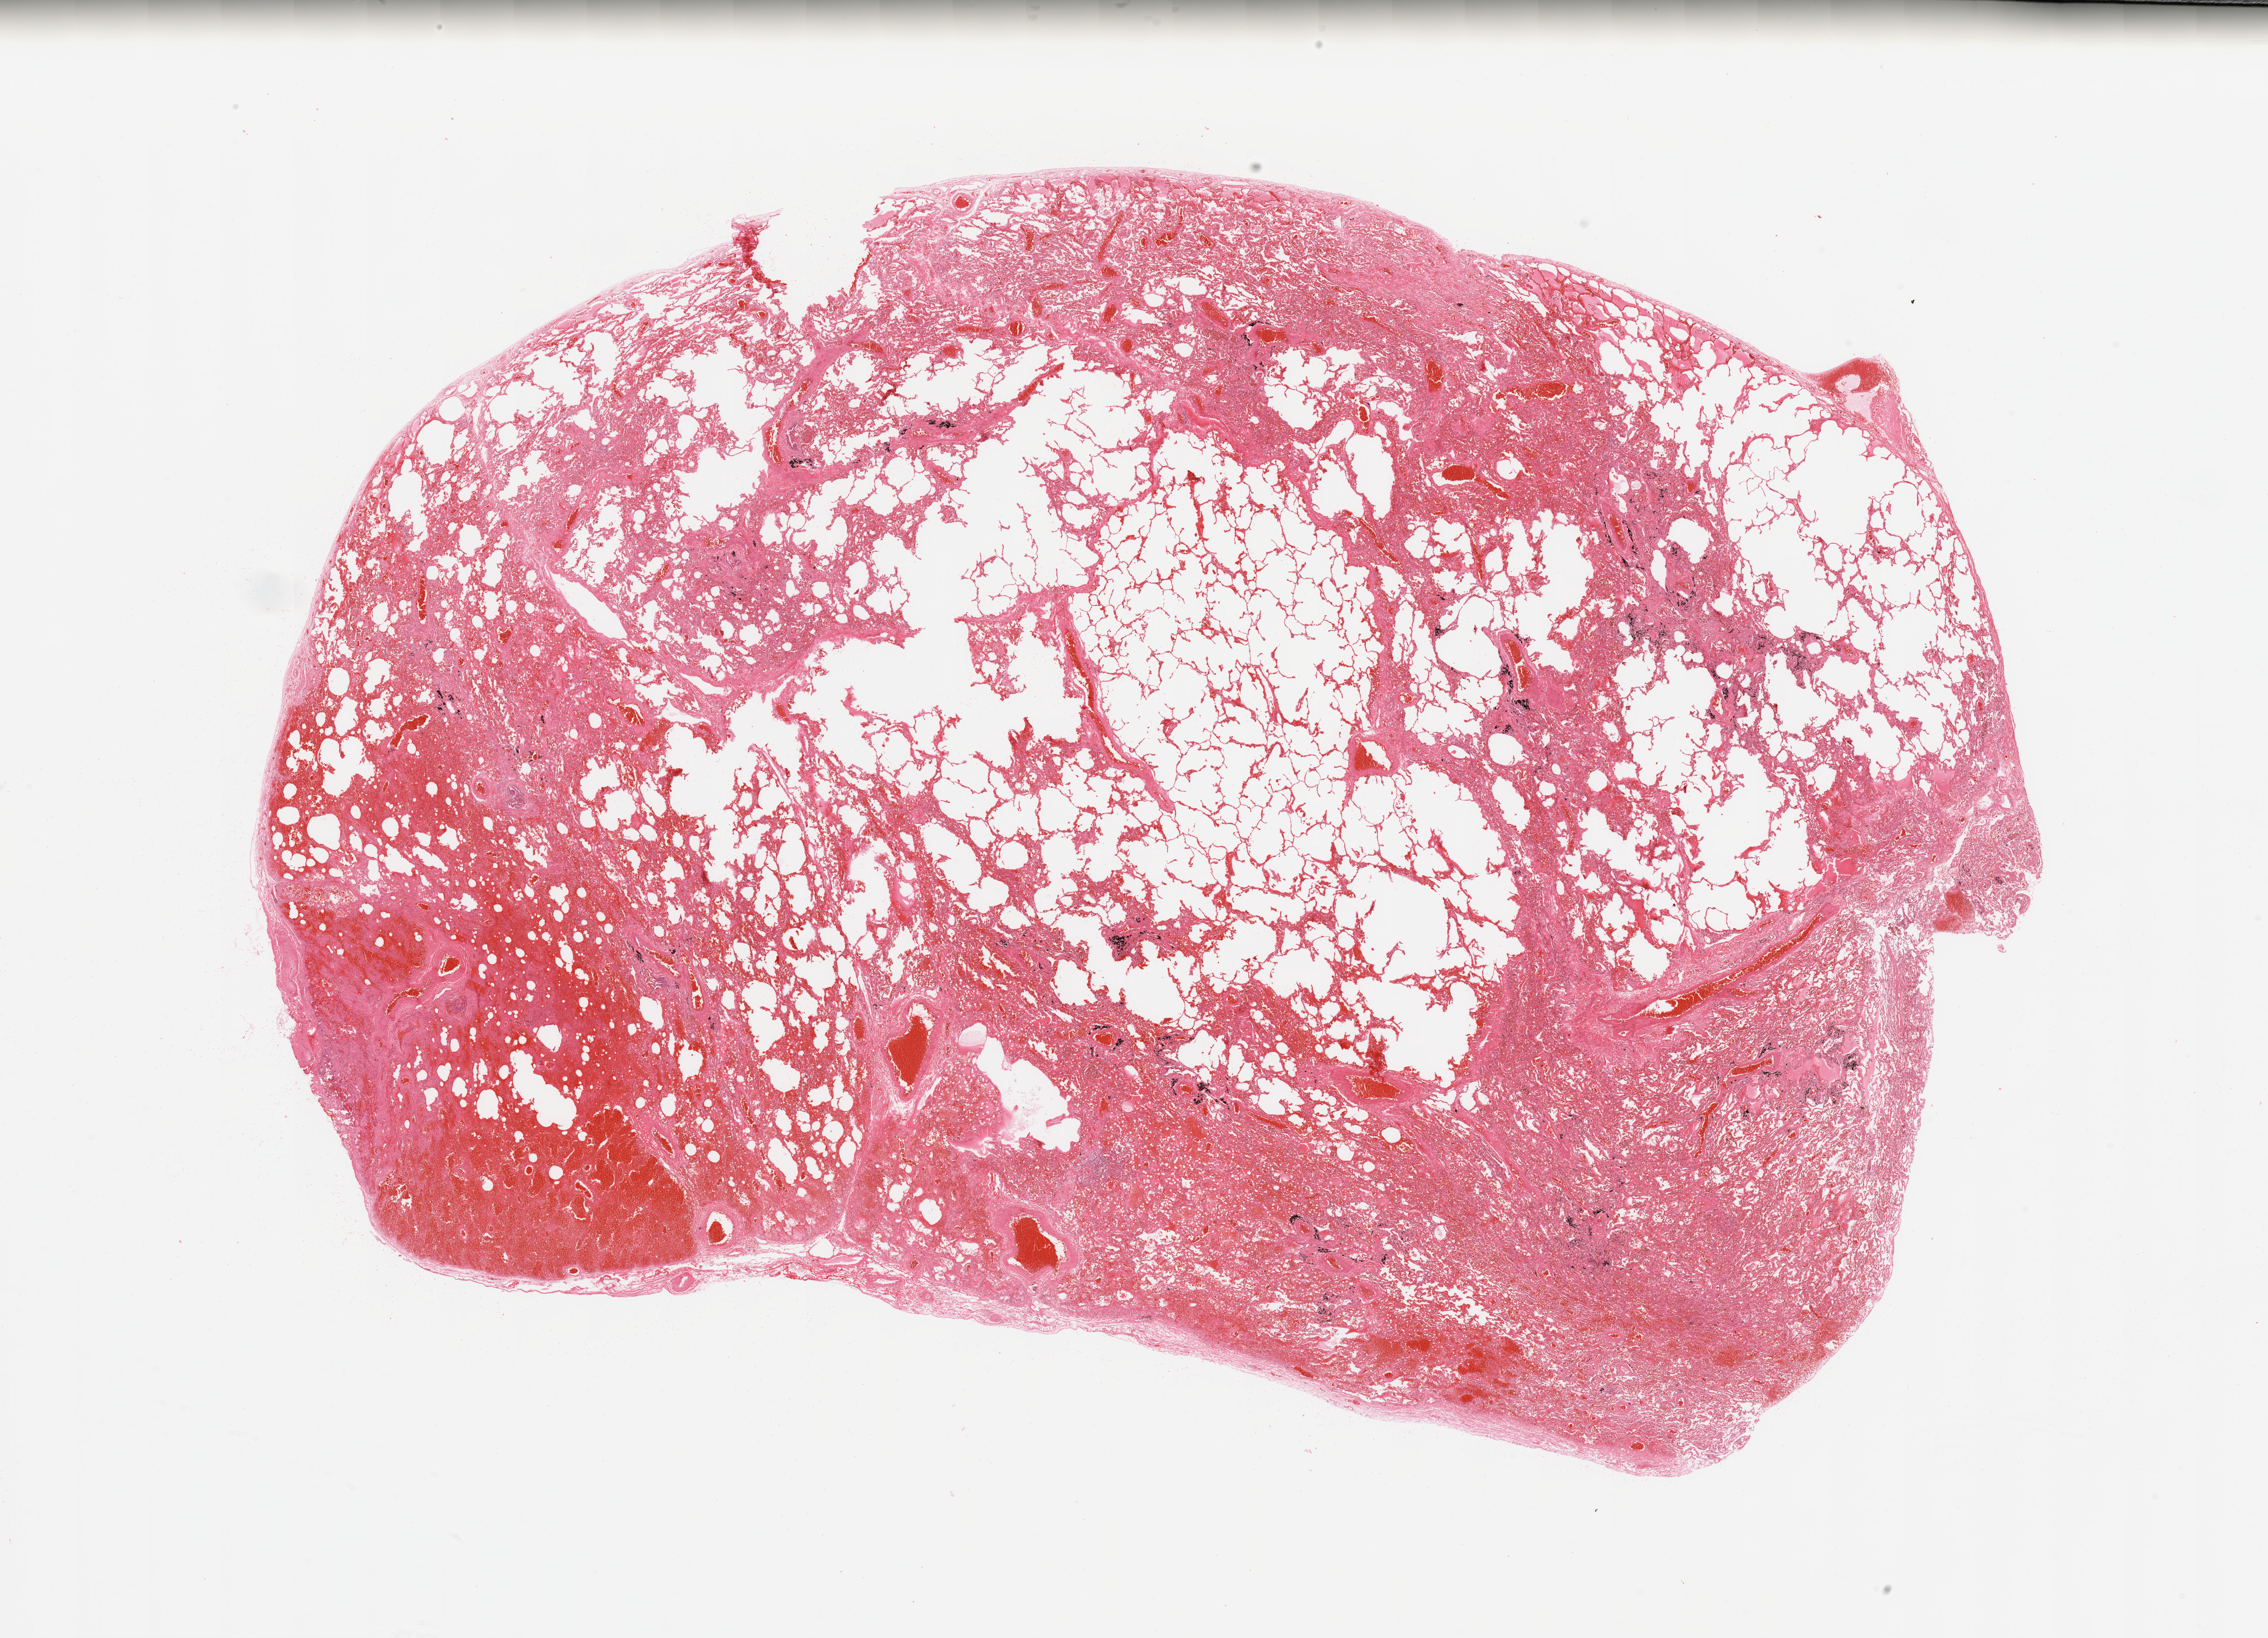
Whole-slide histology image, H&E-stained — whole scanned area (about 30.5 x 22.0 mm) shown as a low-resolution overview; normal (non-tumour) tissue sample, sampled site: lung. 59-year-old male patient.
This section: normal (non-tumour) tissue from the same patient. Patient diagnosis: Adenocarcinoma, NOS.